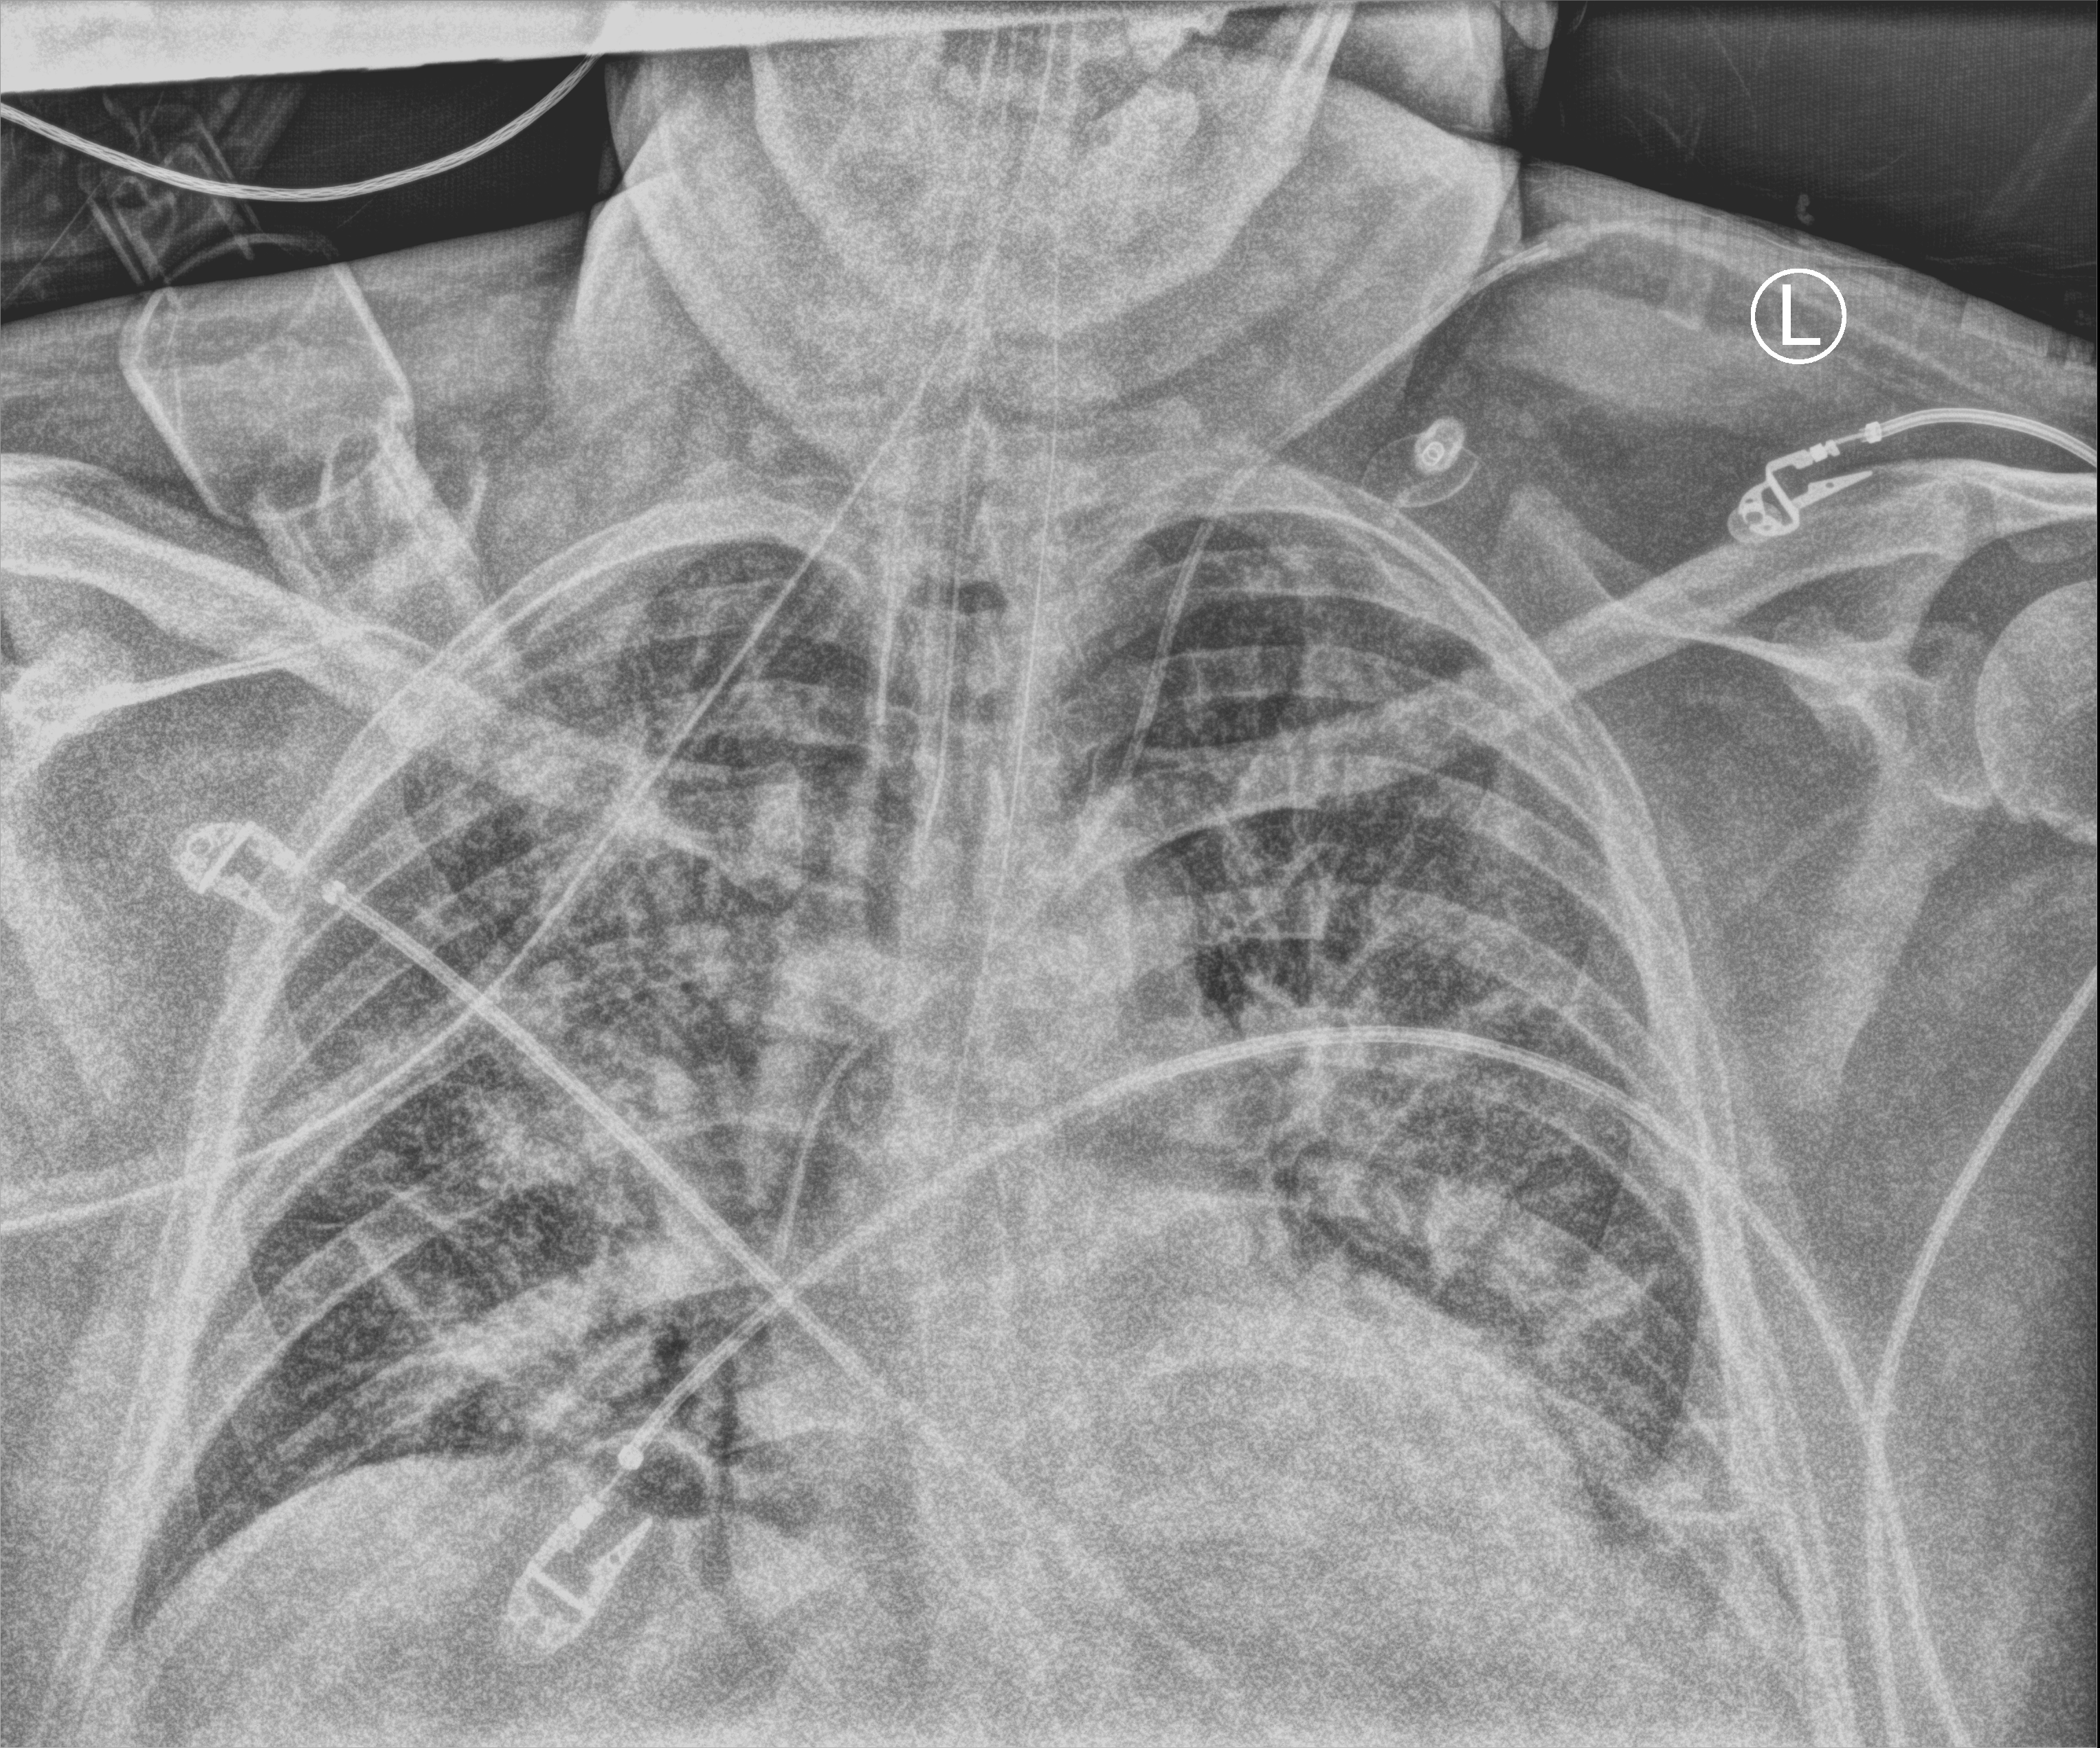
Bedside chest radiograph (computed radiography). Adult patient hospitalised with COVID-19, age 18–59 years.
Hospital-stay facts (about this admission, not read from this image; timing relative to this image not recorded):
- length of hospital stay: 16 days
- chronic kidney disease (admission record): no